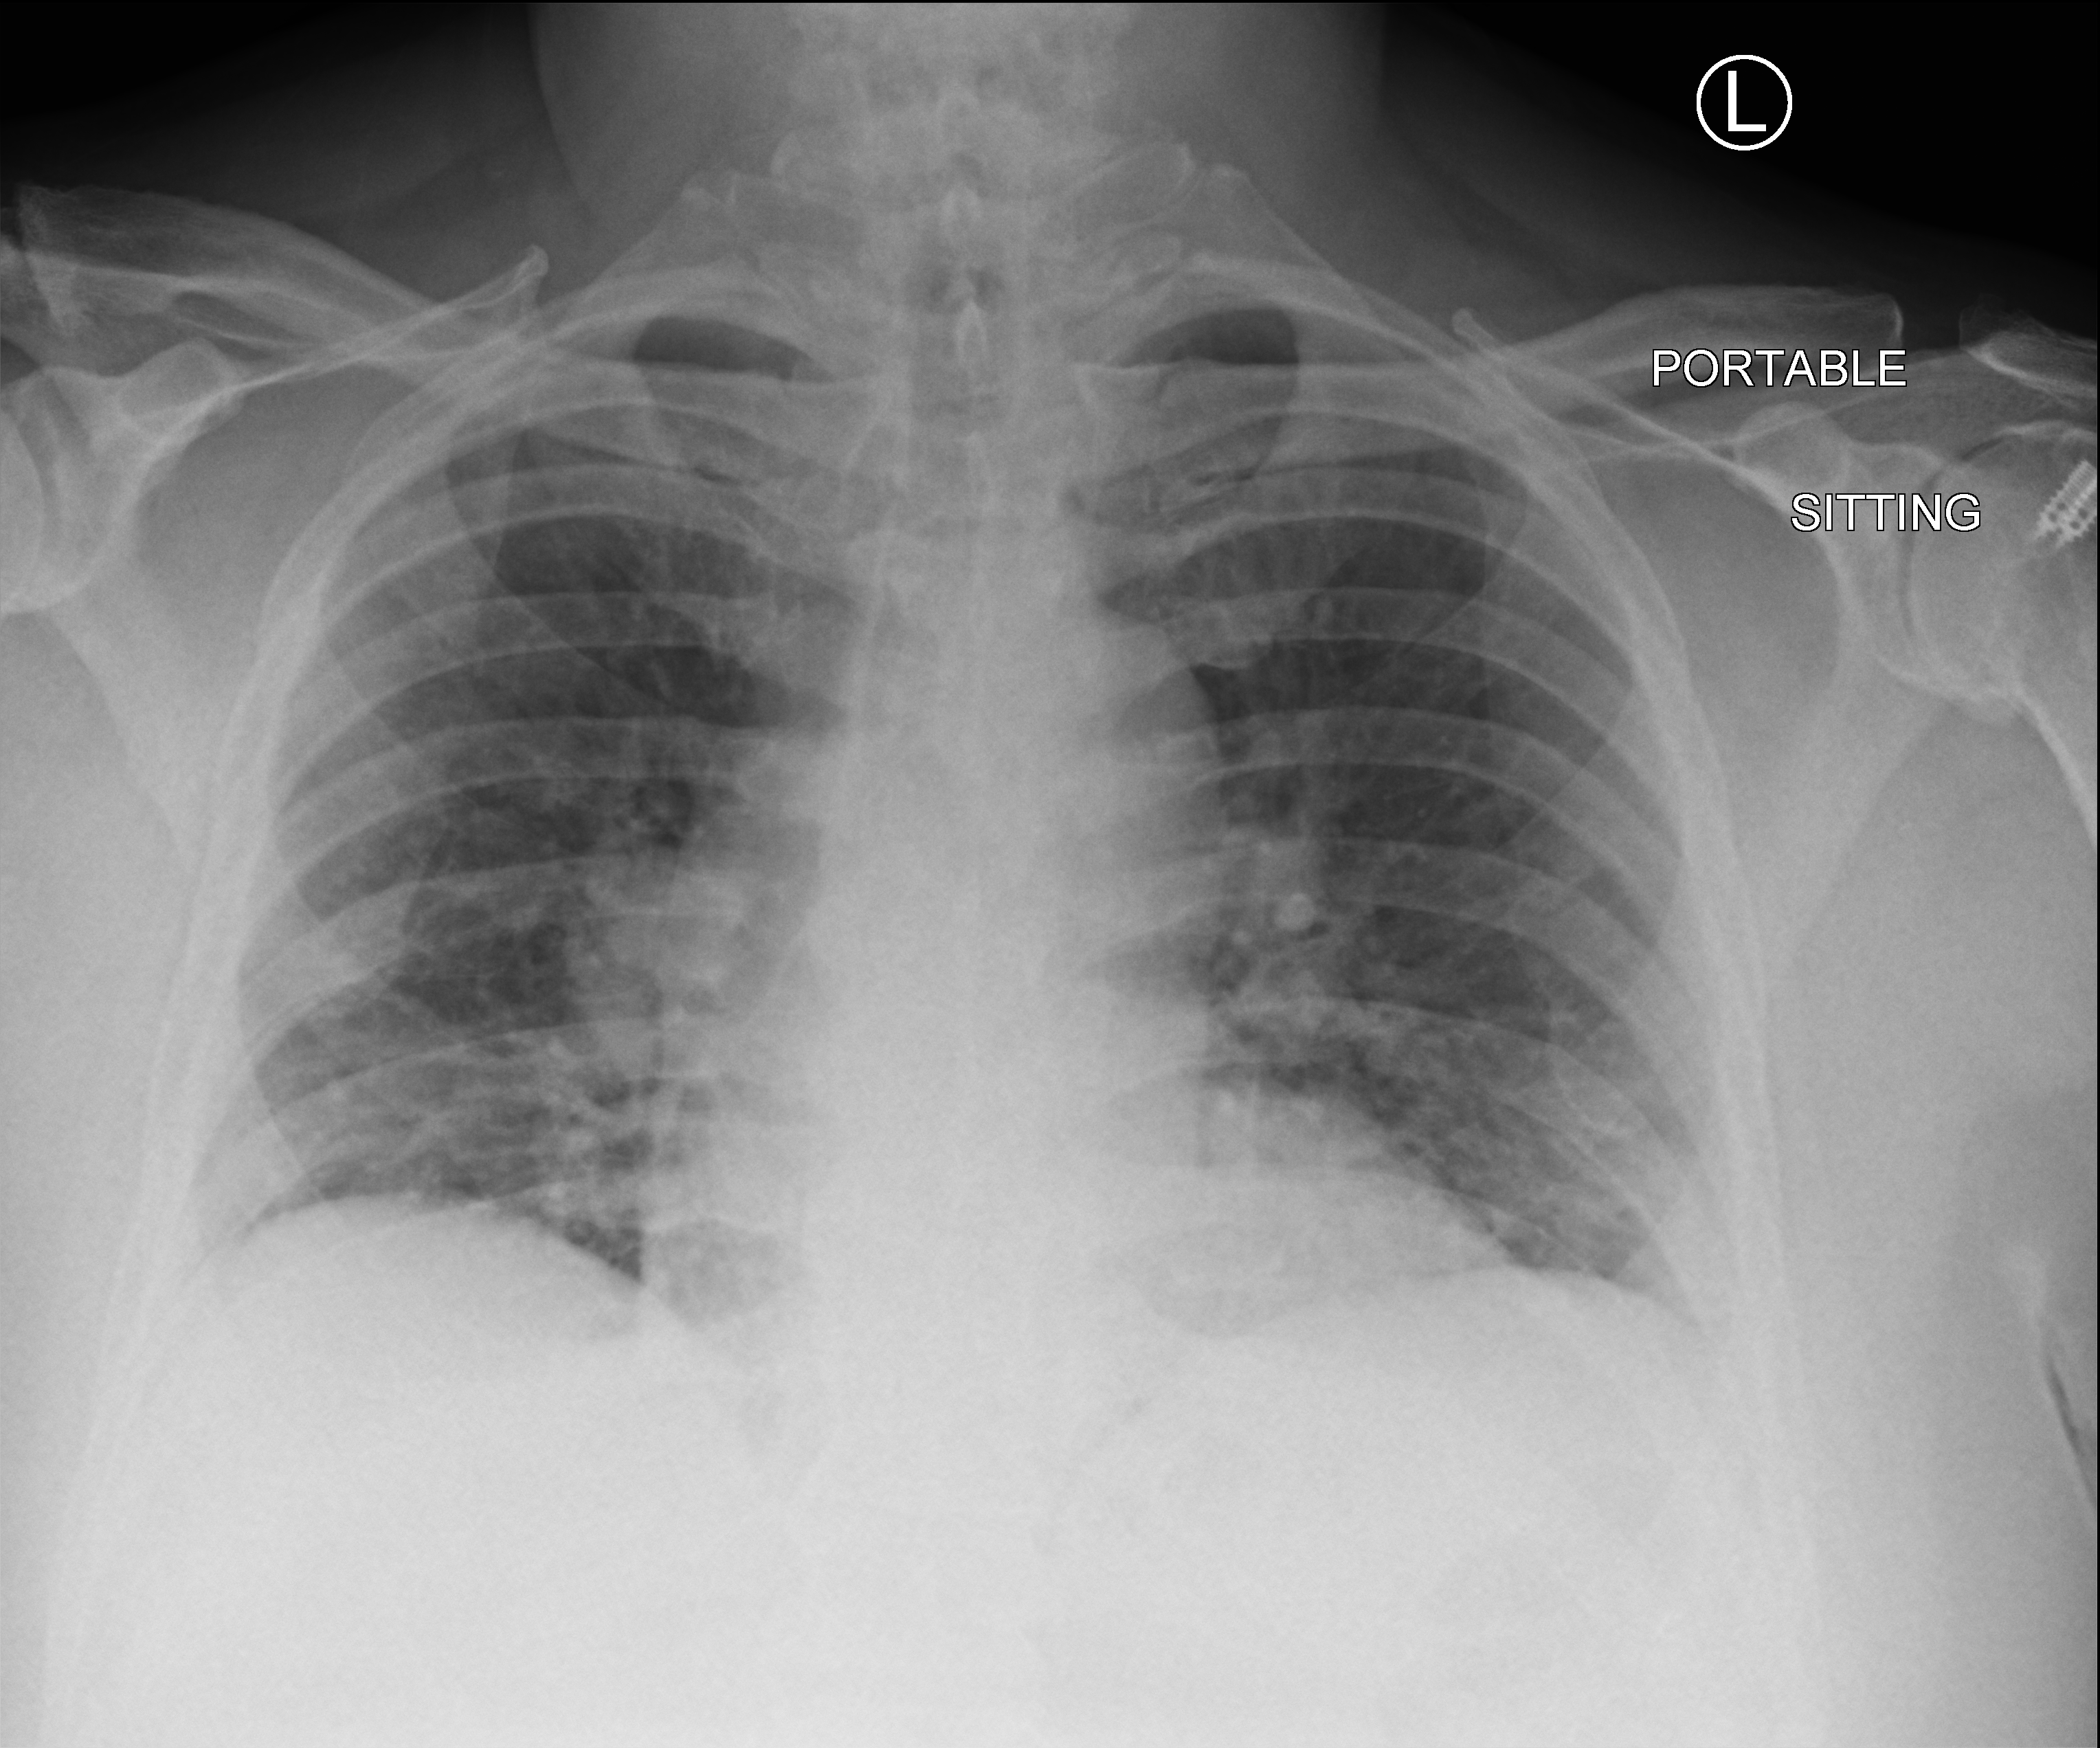
Chest X-ray (portable); anteroposterior (AP) projection. Patient hospitalised with COVID-19; male, aged 60–74 years.
From the hospital-stay record, not from the radiograph (when in the stay this image was taken is not recorded): mechanically ventilated during this hospital stay: no; admitted to intensive care during this hospital stay: no.